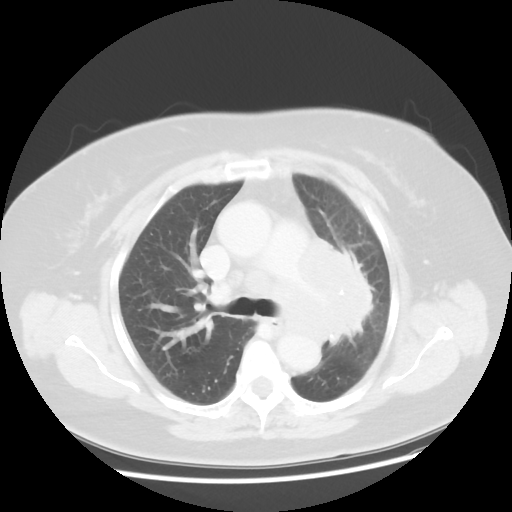
Chest CT, one axial slice; slice 30 of 49 in the series (ordered by position); lung window (W 1500 / L -600 HU); 5 mm slice thickness; 512 × 512 image matrix. Female patient, age 58 years. From the clinical record (not read from this slice): clinical TNM (as recorded): T4 N3 M0.
Annotated regions visible in this slice (rectangle marked by the reading radiologist):
- lung tumour (recorded histology: small cell carcinoma): bounding box (x1, y1, x2, y2) in pixels: (265, 215, 378, 353)